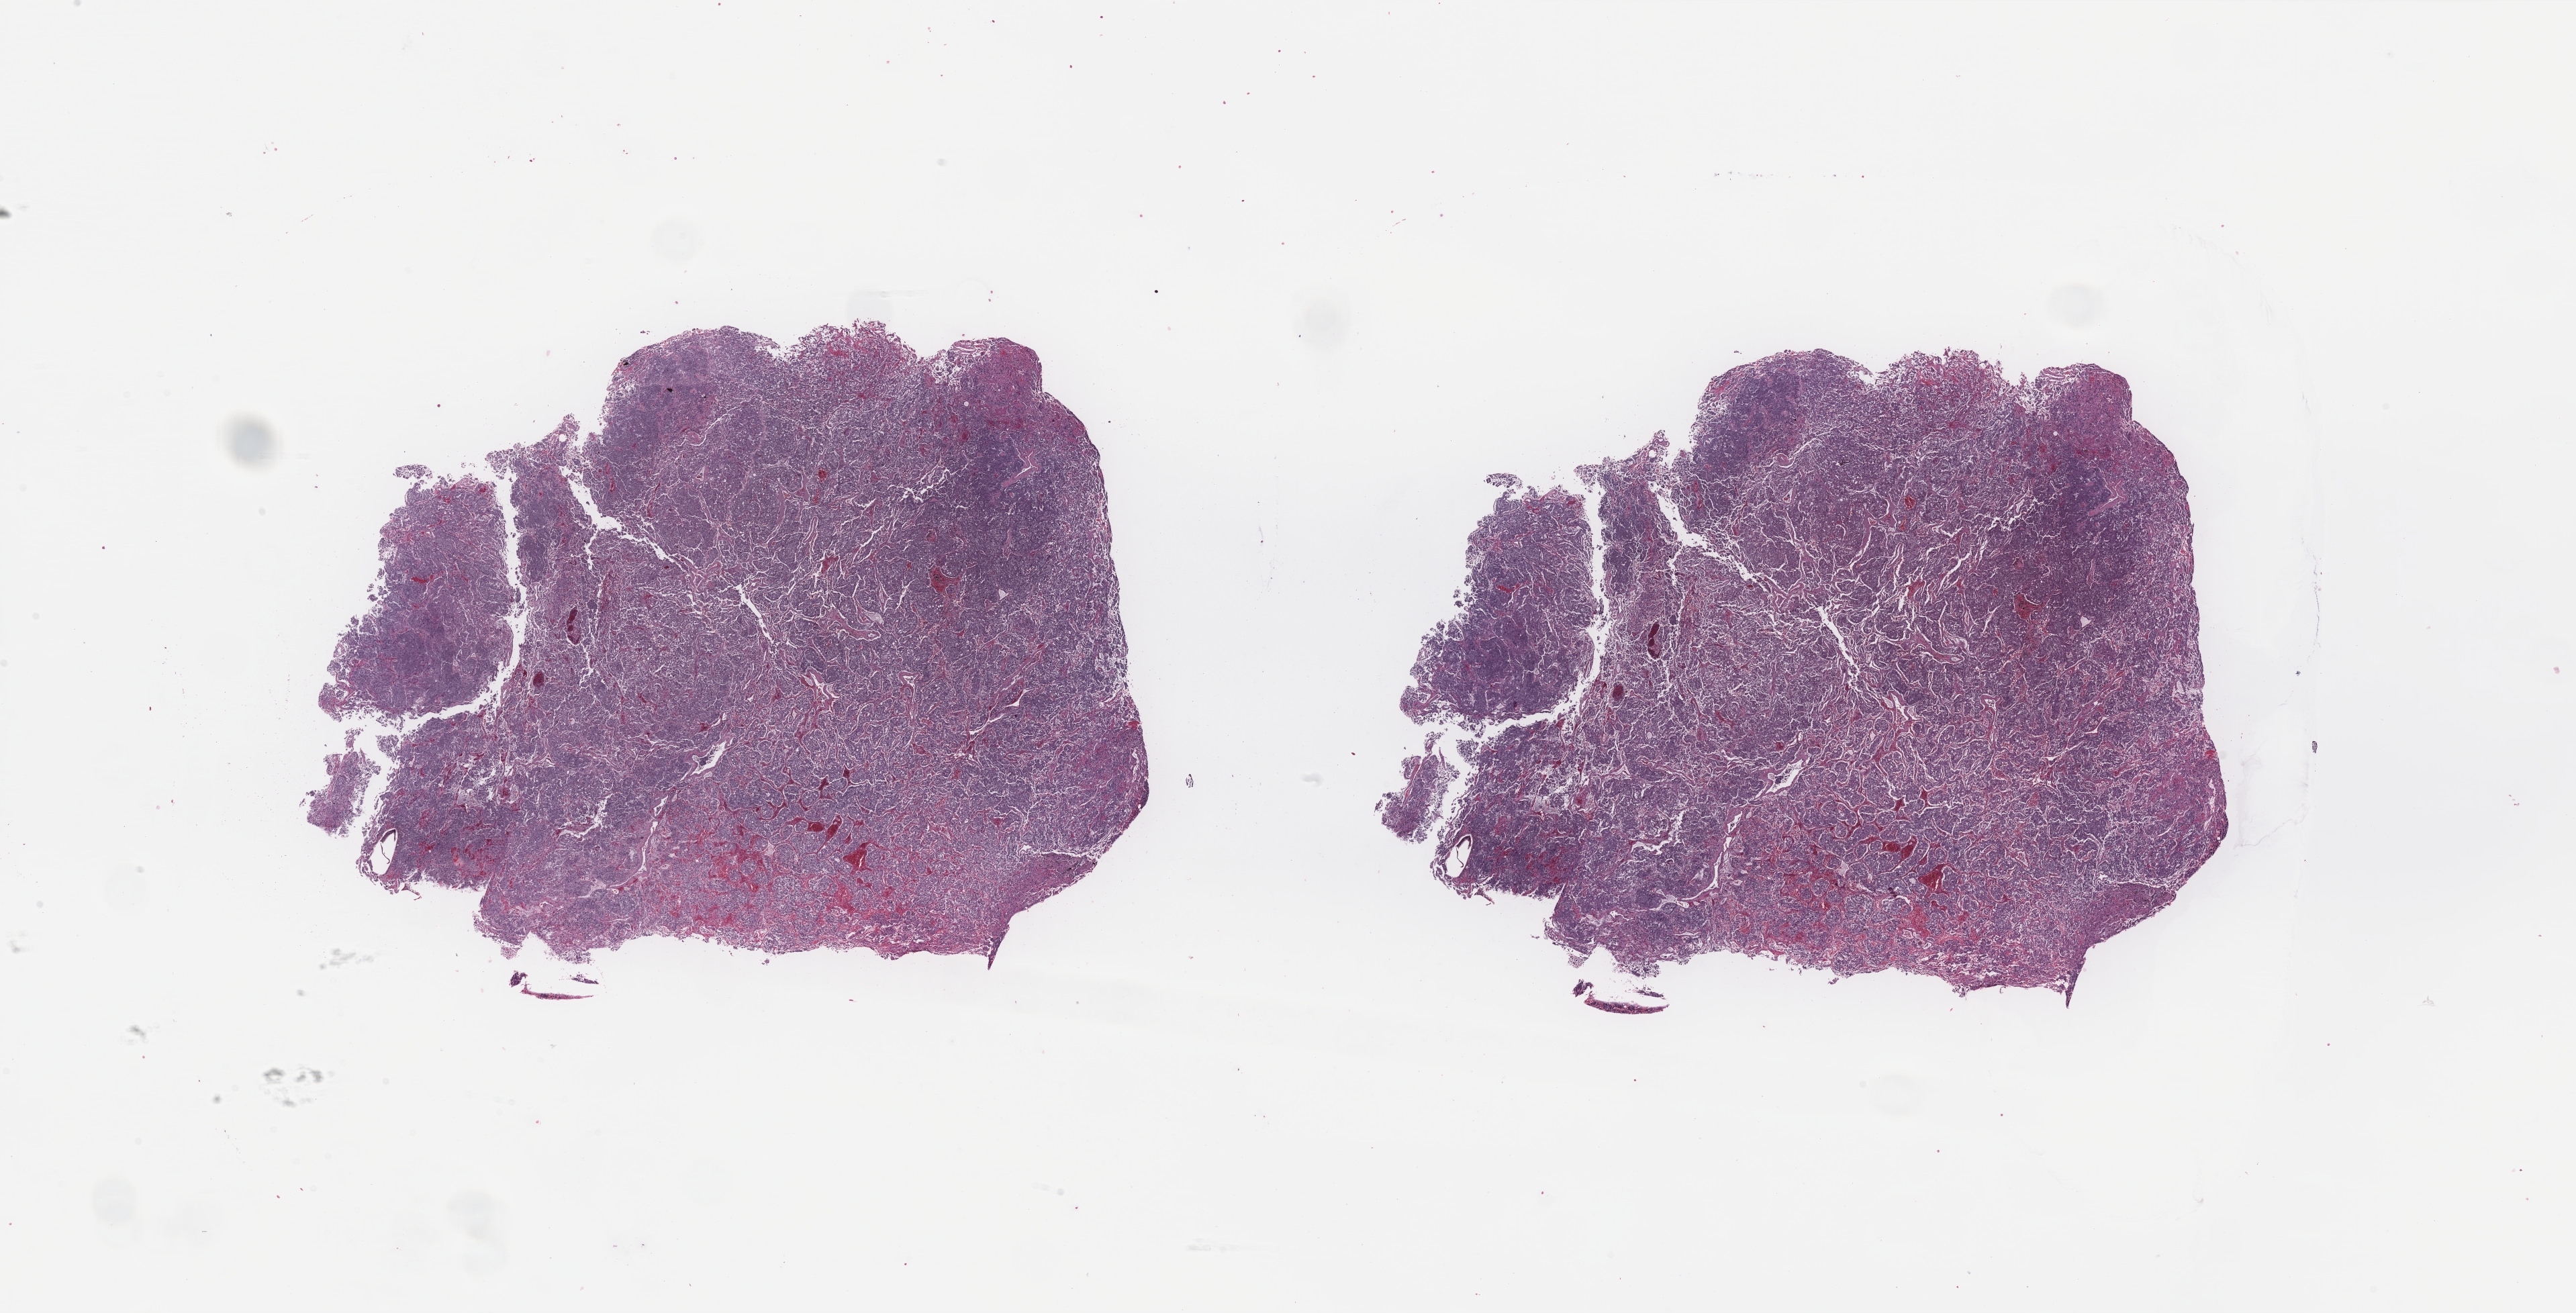
H&E-stained whole-slide image, a low-resolution overview of the entire scanned area, about 30.4 x 15.5 mm (acquisition: 40x scan), FFPE section, sample: primary tumour, adrenal gland. Male patient; age at initial diagnosis 43 years.
• diagnosis: Pheochromocytoma, malignant
• laterality: left